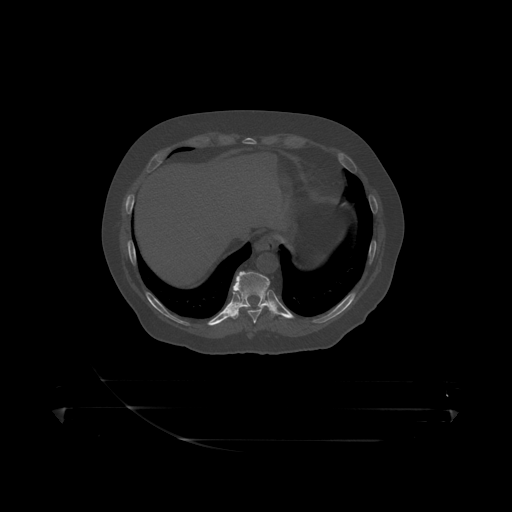
CT including the spine, one axial slice; position 226 of 390 along the scan axis; 120 kVp; bone window (W 1800 / L 400 HU); 1.25 mm slice thickness; 512 × 512 image matrix, field of view 650 × 650 mm. Male patient, age 60 years. From the clinical record (not read from this slice): primary cancer: prostate.
Annotated regions visible in this slice (semi-automatic segmentation, software-assisted and operator-edited):
- T10 vertebra: bounding box (x1, y1, x2, y2) in pixels: (236, 272, 275, 316)
- T9 vertebra: (233, 285, 269, 319)